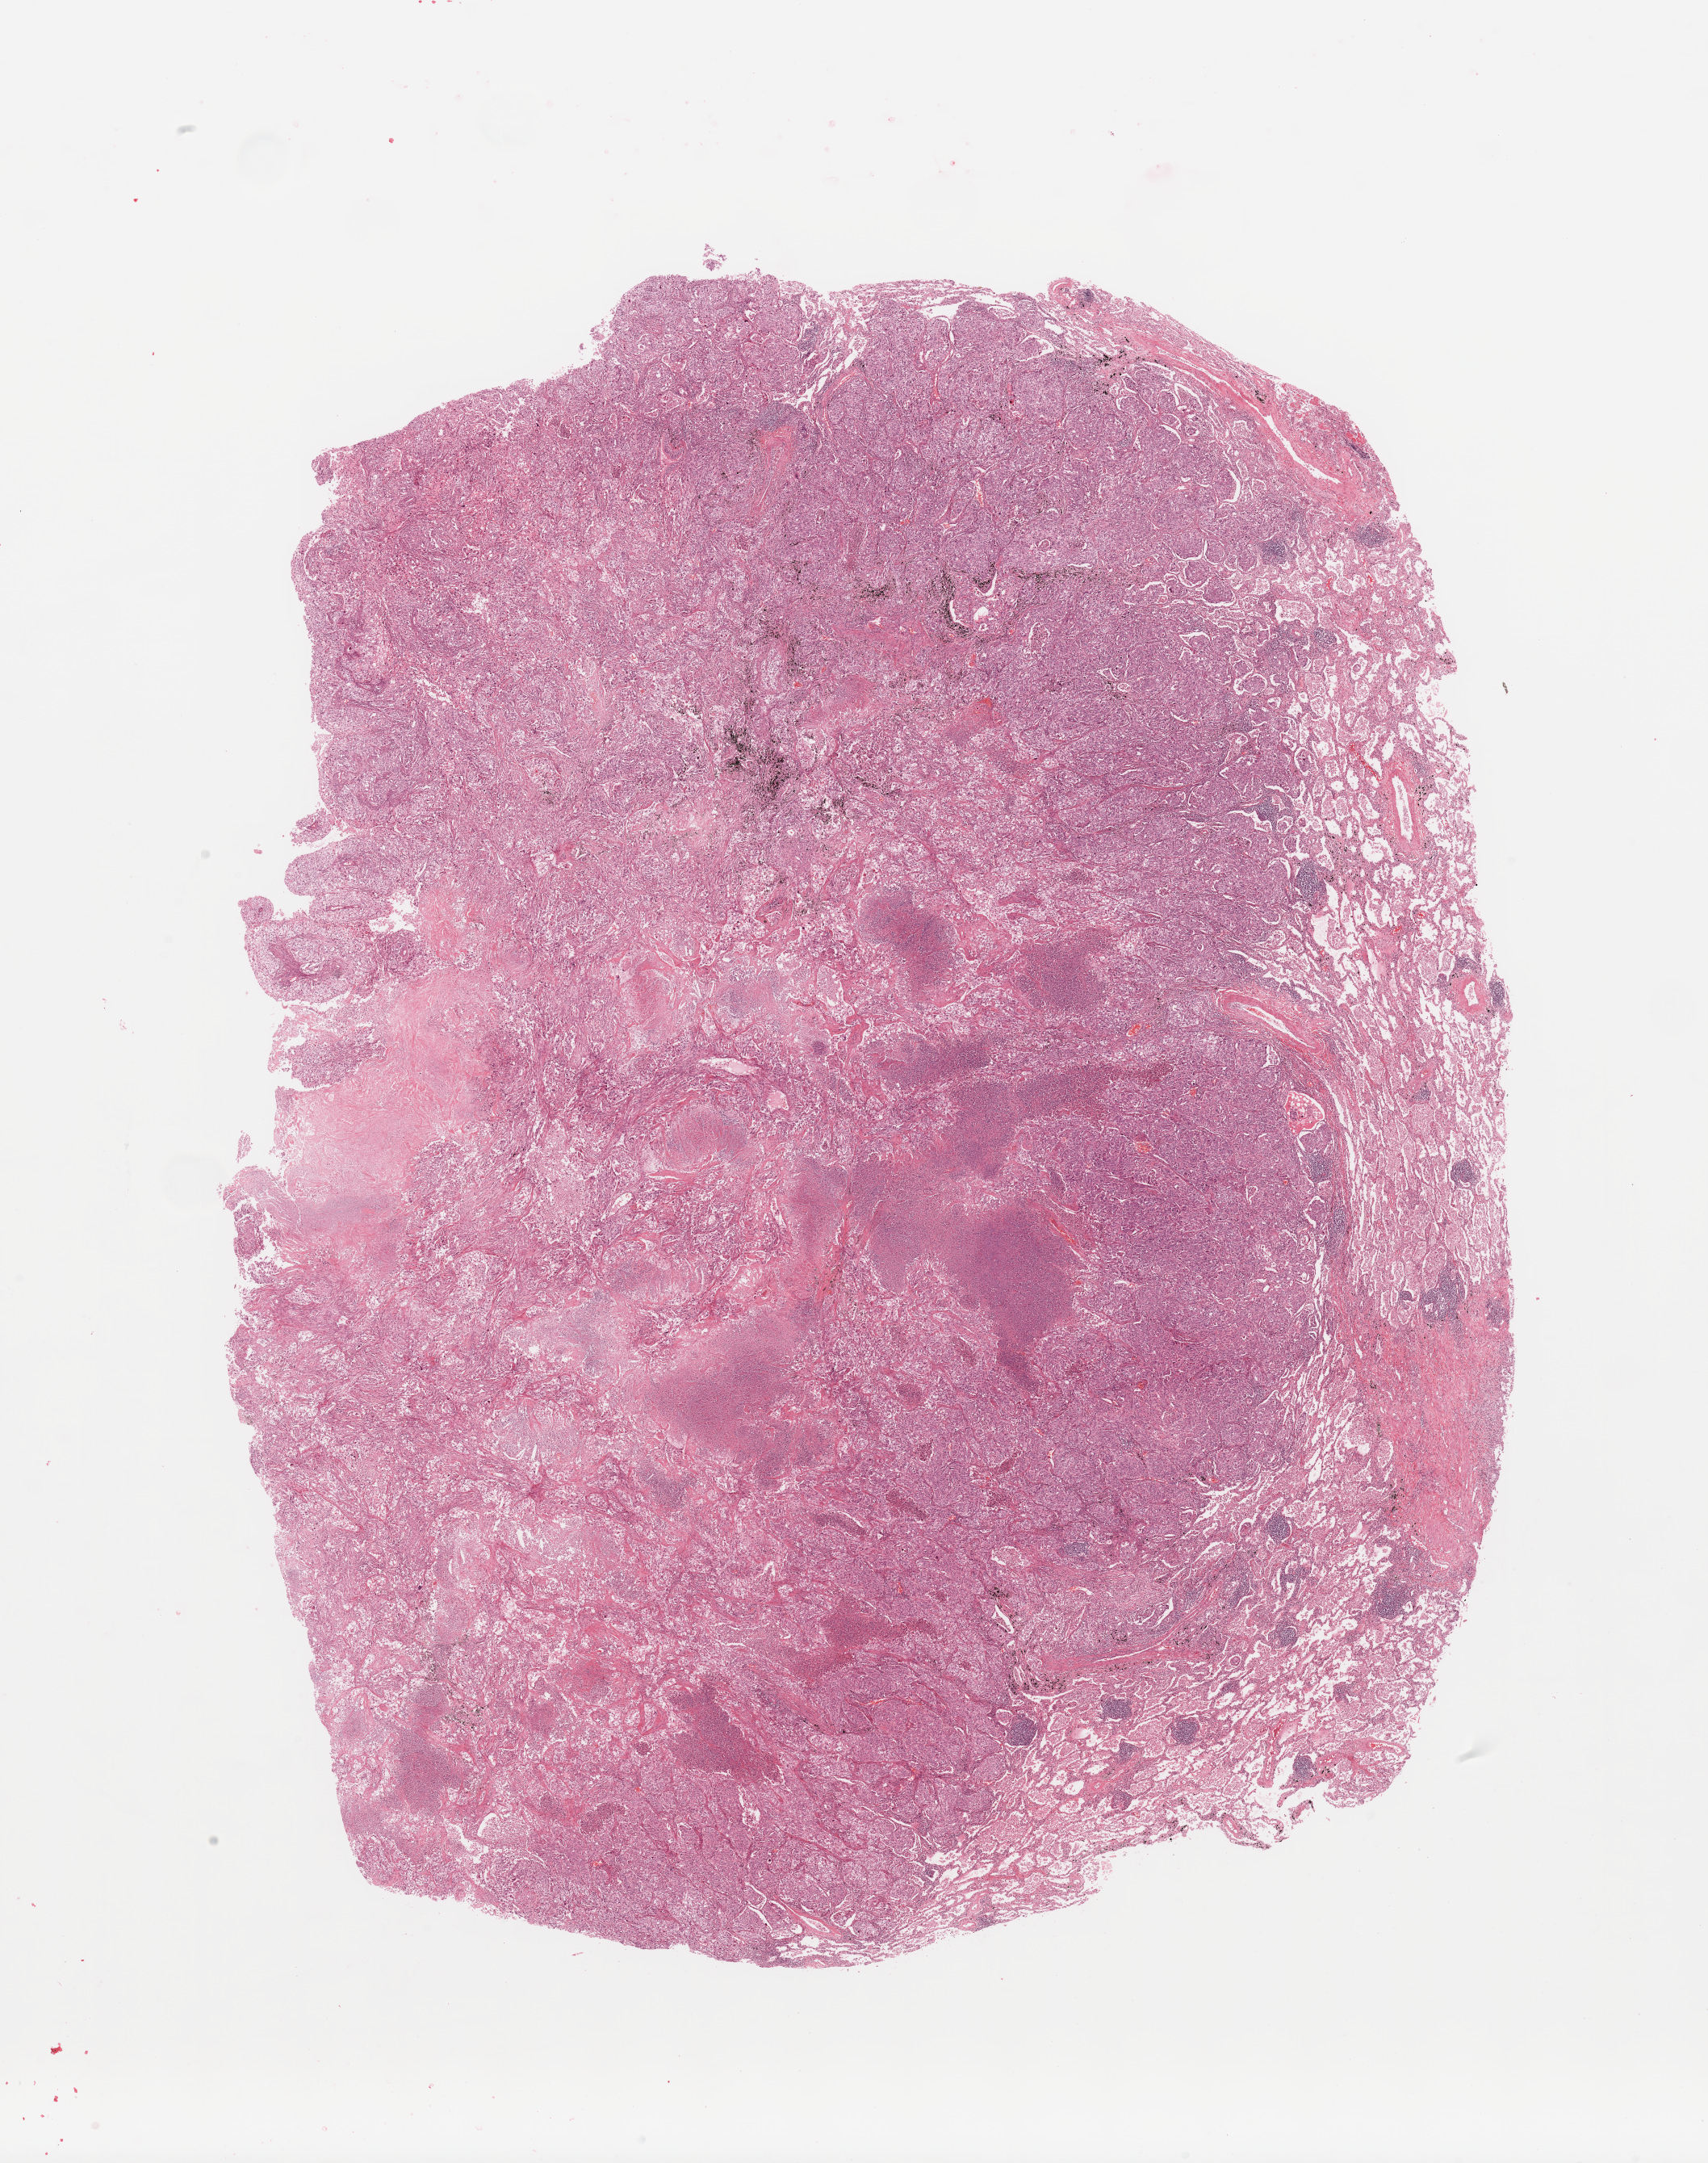
H&E-stained whole-slide image, whole scanned area (about 16.7 x 21.2 mm, slide scanned at 20x) shown as a low-resolution overview; lung, tumour tissue. Patient: male, age 69 years. Histologic grade: G3 (poorly differentiated).
Histologic diagnosis: Adenocarcinoma, NOS. AJCC pathologic stage: IIB.